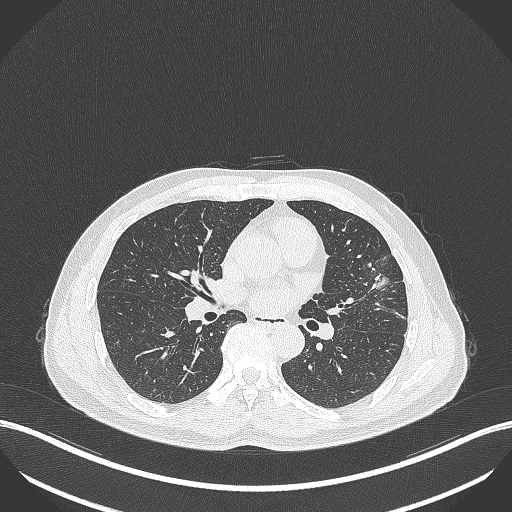
Chest CT, one axial slice. Slice 204 of 418 in the series (ordered by position). 120 kVp. Lung window (W 1500 / L -600 HU). 512 × 512 image matrix. Male patient, age 55 years. From the clinical record (not read from this slice): clinical TNM (as recorded): T1c N0 M0; histopathological grade: G2-3.
Outlined on this slice (bounding box drawn by a radiologist):
- lung tumour (recorded histology: adenocarcinoma): bounding box (x1, y1, x2, y2) in pixels: (369, 269, 396, 298)